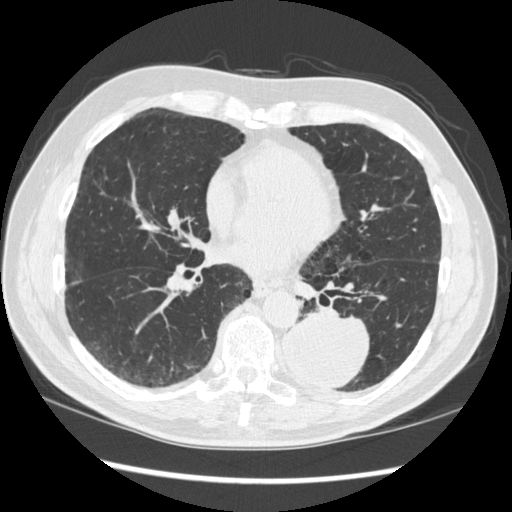
Low-dose screening chest CT, one axial slice; slice 145 of 348 in the series (ordered by position); reconstruction kernel STANDARD; 120 kVp; lung window (W 1500 / L -600 HU); 512 × 512 image matrix, field of view 360 × 360 mm.
Outlined on this slice (outlined manually by an expert reader):
- lesion 1 (tumor, lower lobe of left lung): bounding box [x1, y1, x2, y2] px = [283, 311, 369, 390]